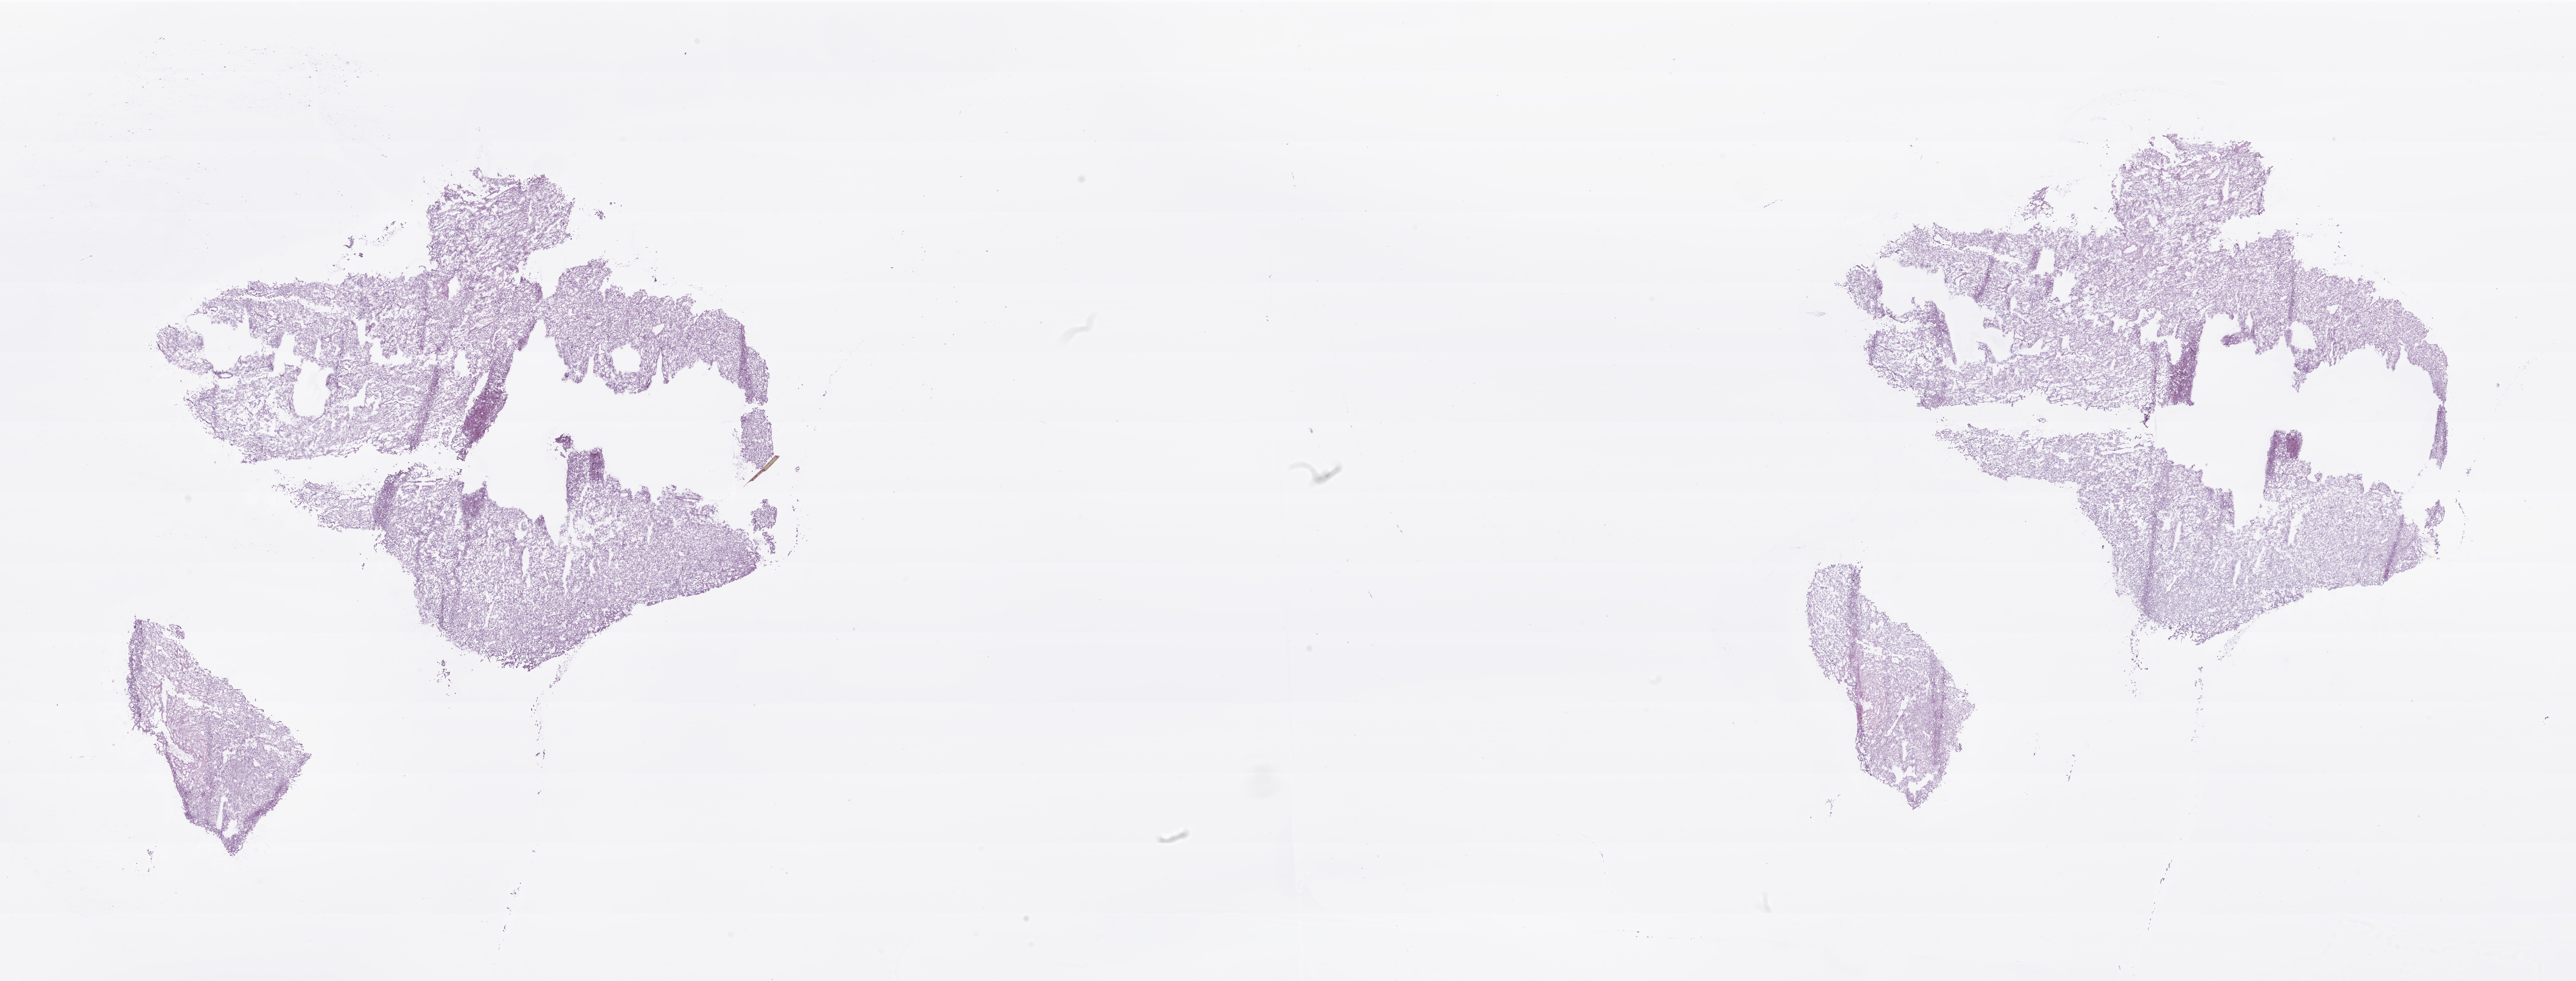
Digitized haematoxylin and eosin-stained section of tumor tissue from the adrenal gland — whole scanned area (about 39.1 x 14.9 mm) shown as a low-resolution overview. Frozen section (OCT-embedded). Patient female; age 133 months (11 years 1 month).
Recorded diagnosis: Pheochromocytoma, NOS.